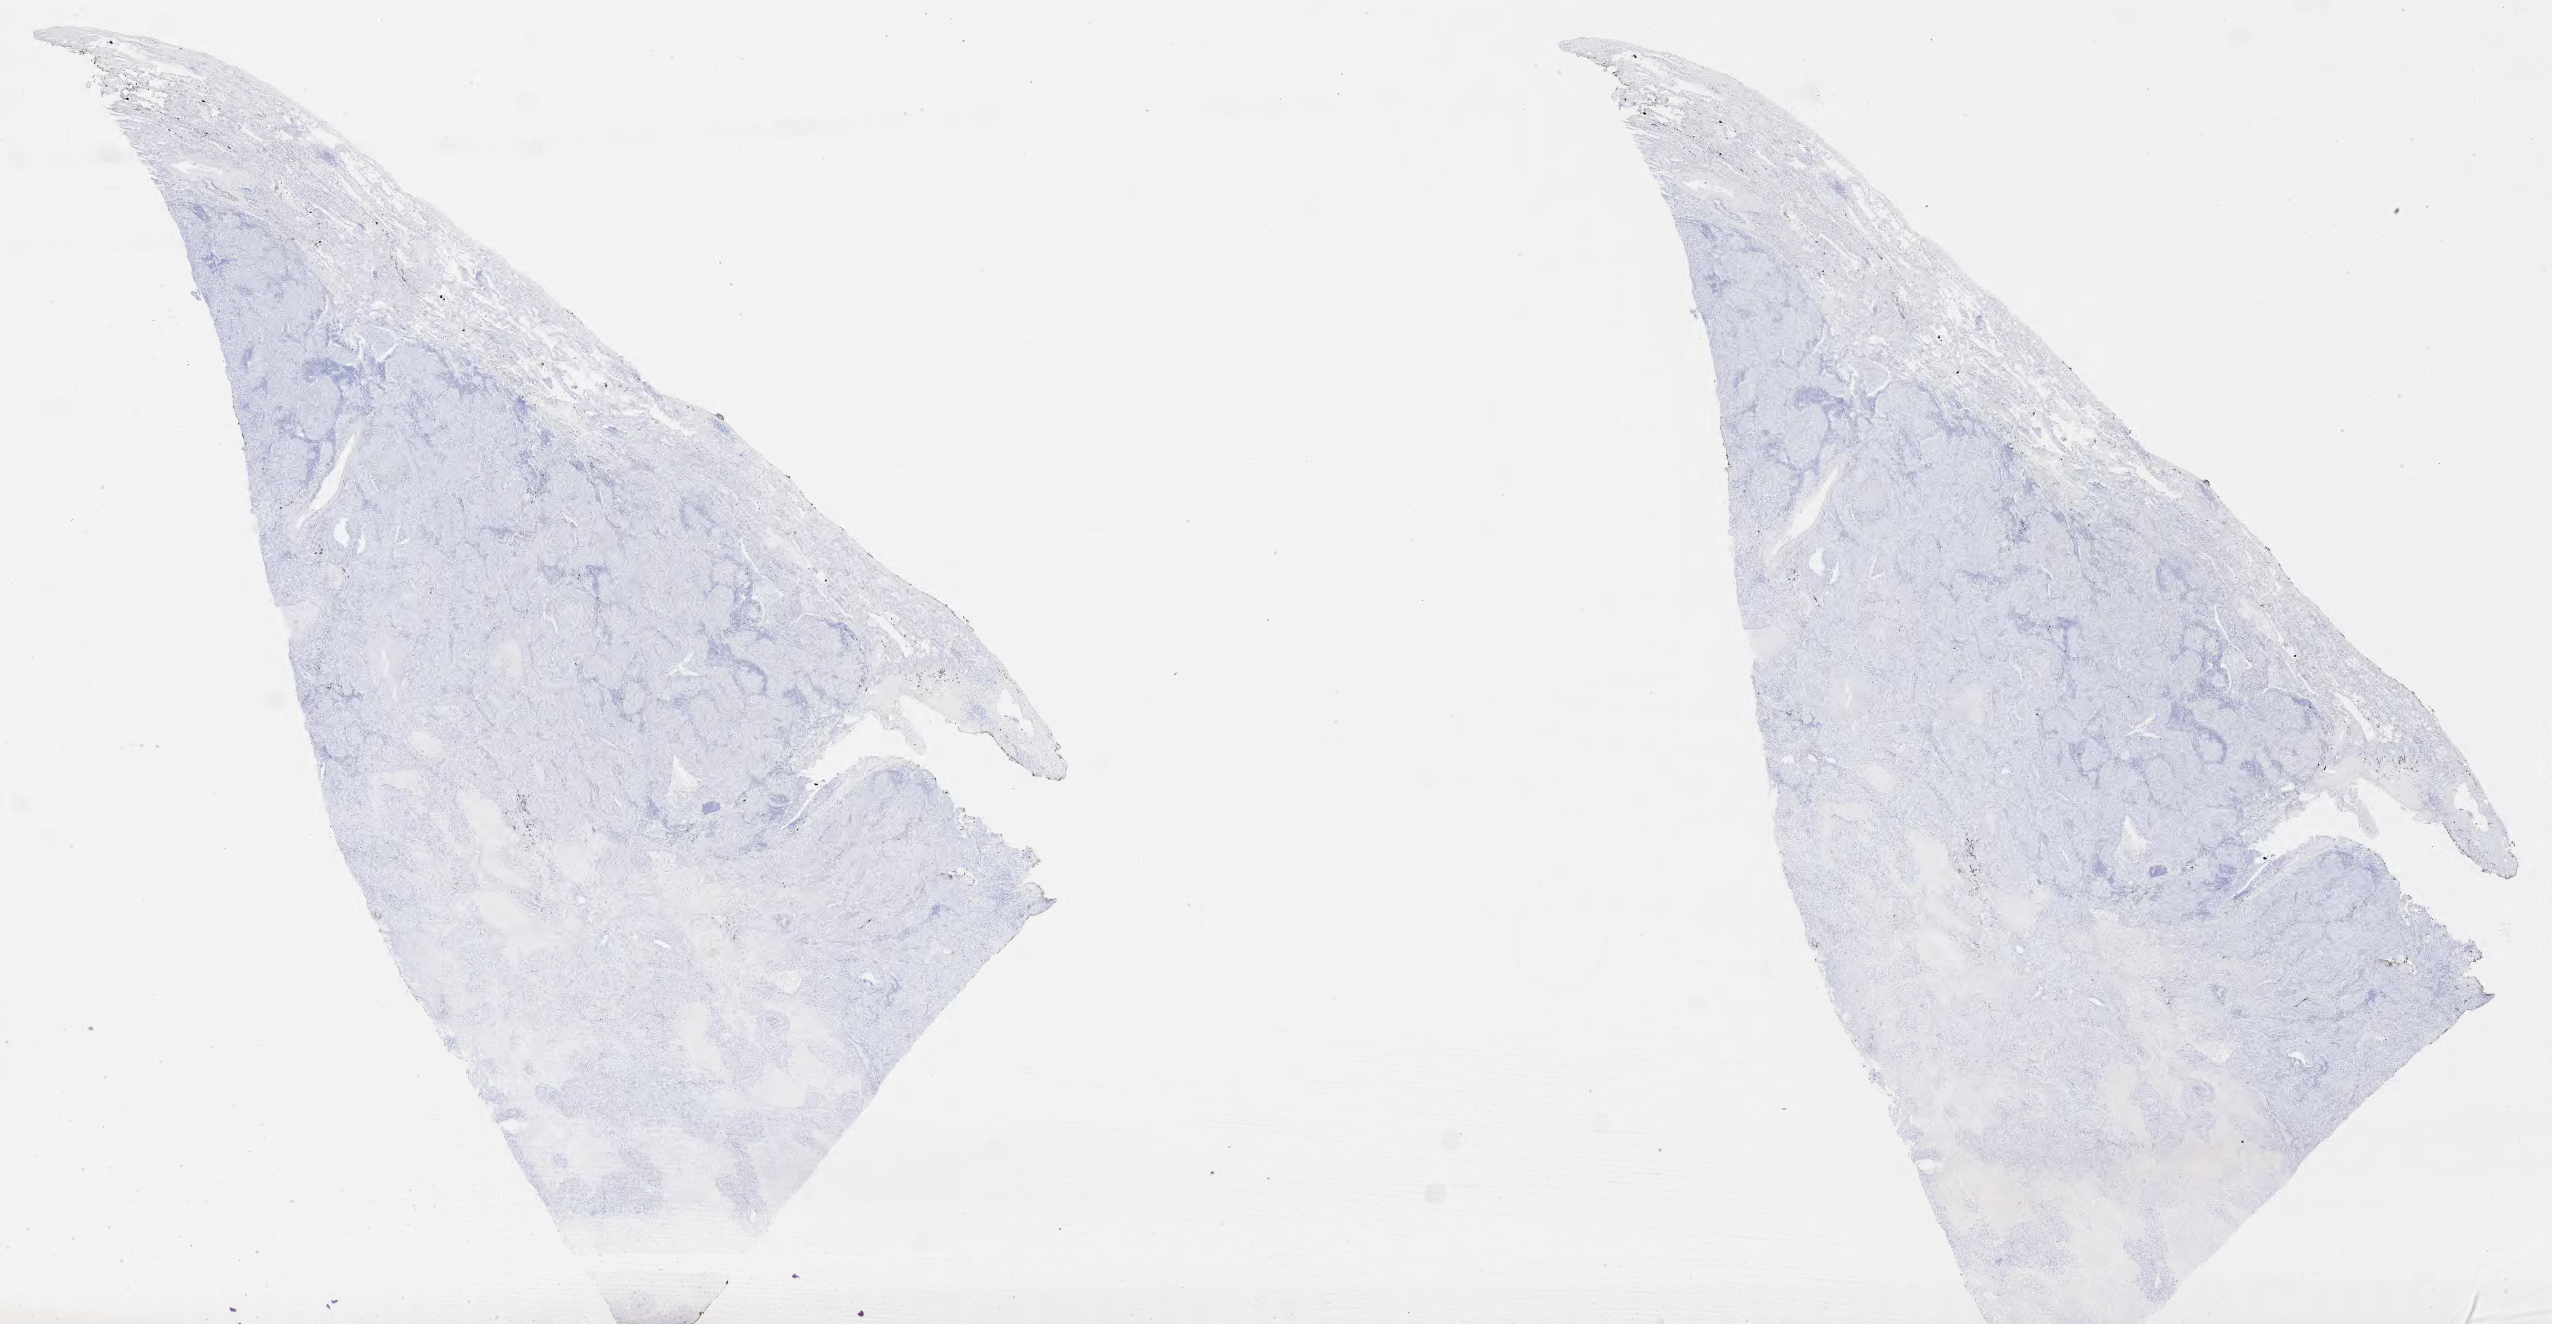
Whole-slide image, immunohistochemical stain for p40, low-resolution overview of the scanned area, about 41.3 x 21.4 mm. Tumor tissue. Anatomic site: lung (left). Patient: female, 69 years old.
• diagnosis: Squamous cell carcinoma, NOS